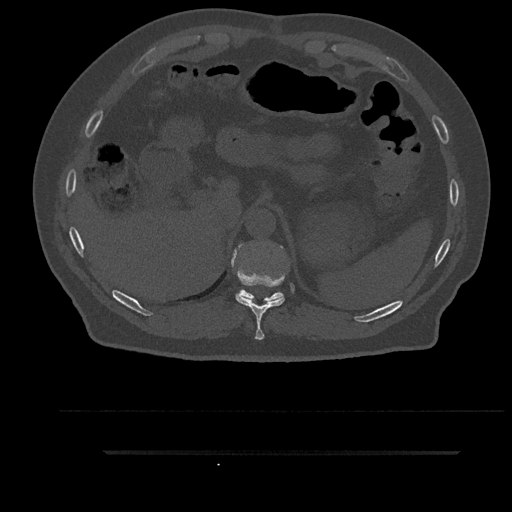
CT including the spine, one axial slice. Position 341 of 797 along the scan axis. 120 kVp. Bone window (W 1800 / L 400 HU). 0.5 mm slice thickness. 512 × 512 image matrix. Patient: male, 63 years. From the clinical record (not read from this slice): primary cancer: renal.
Annotated regions visible in this slice (semi-automatic segmentation, software-assisted and operator-edited):
- T10 vertebra: box from (x=231, y=244) to (x=285, y=340) px
- T11 vertebra: (x=237, y=290)–(x=284, y=303)